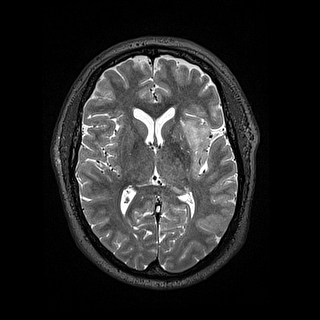
Brain MRI from a brain-tumour surgery series, one axial slice; 1.2 mm slice thickness; 320 × 320 image matrix. From the clinical record (not read from this slice): histopathology: Astrocytoma; WHO grade: 2; IDH mutation: yes; tumour location: Left Insular.
Annotated regions visible in this slice (expert manual segmentation):
- tumour: box from (x=182, y=122) to (x=211, y=177) px